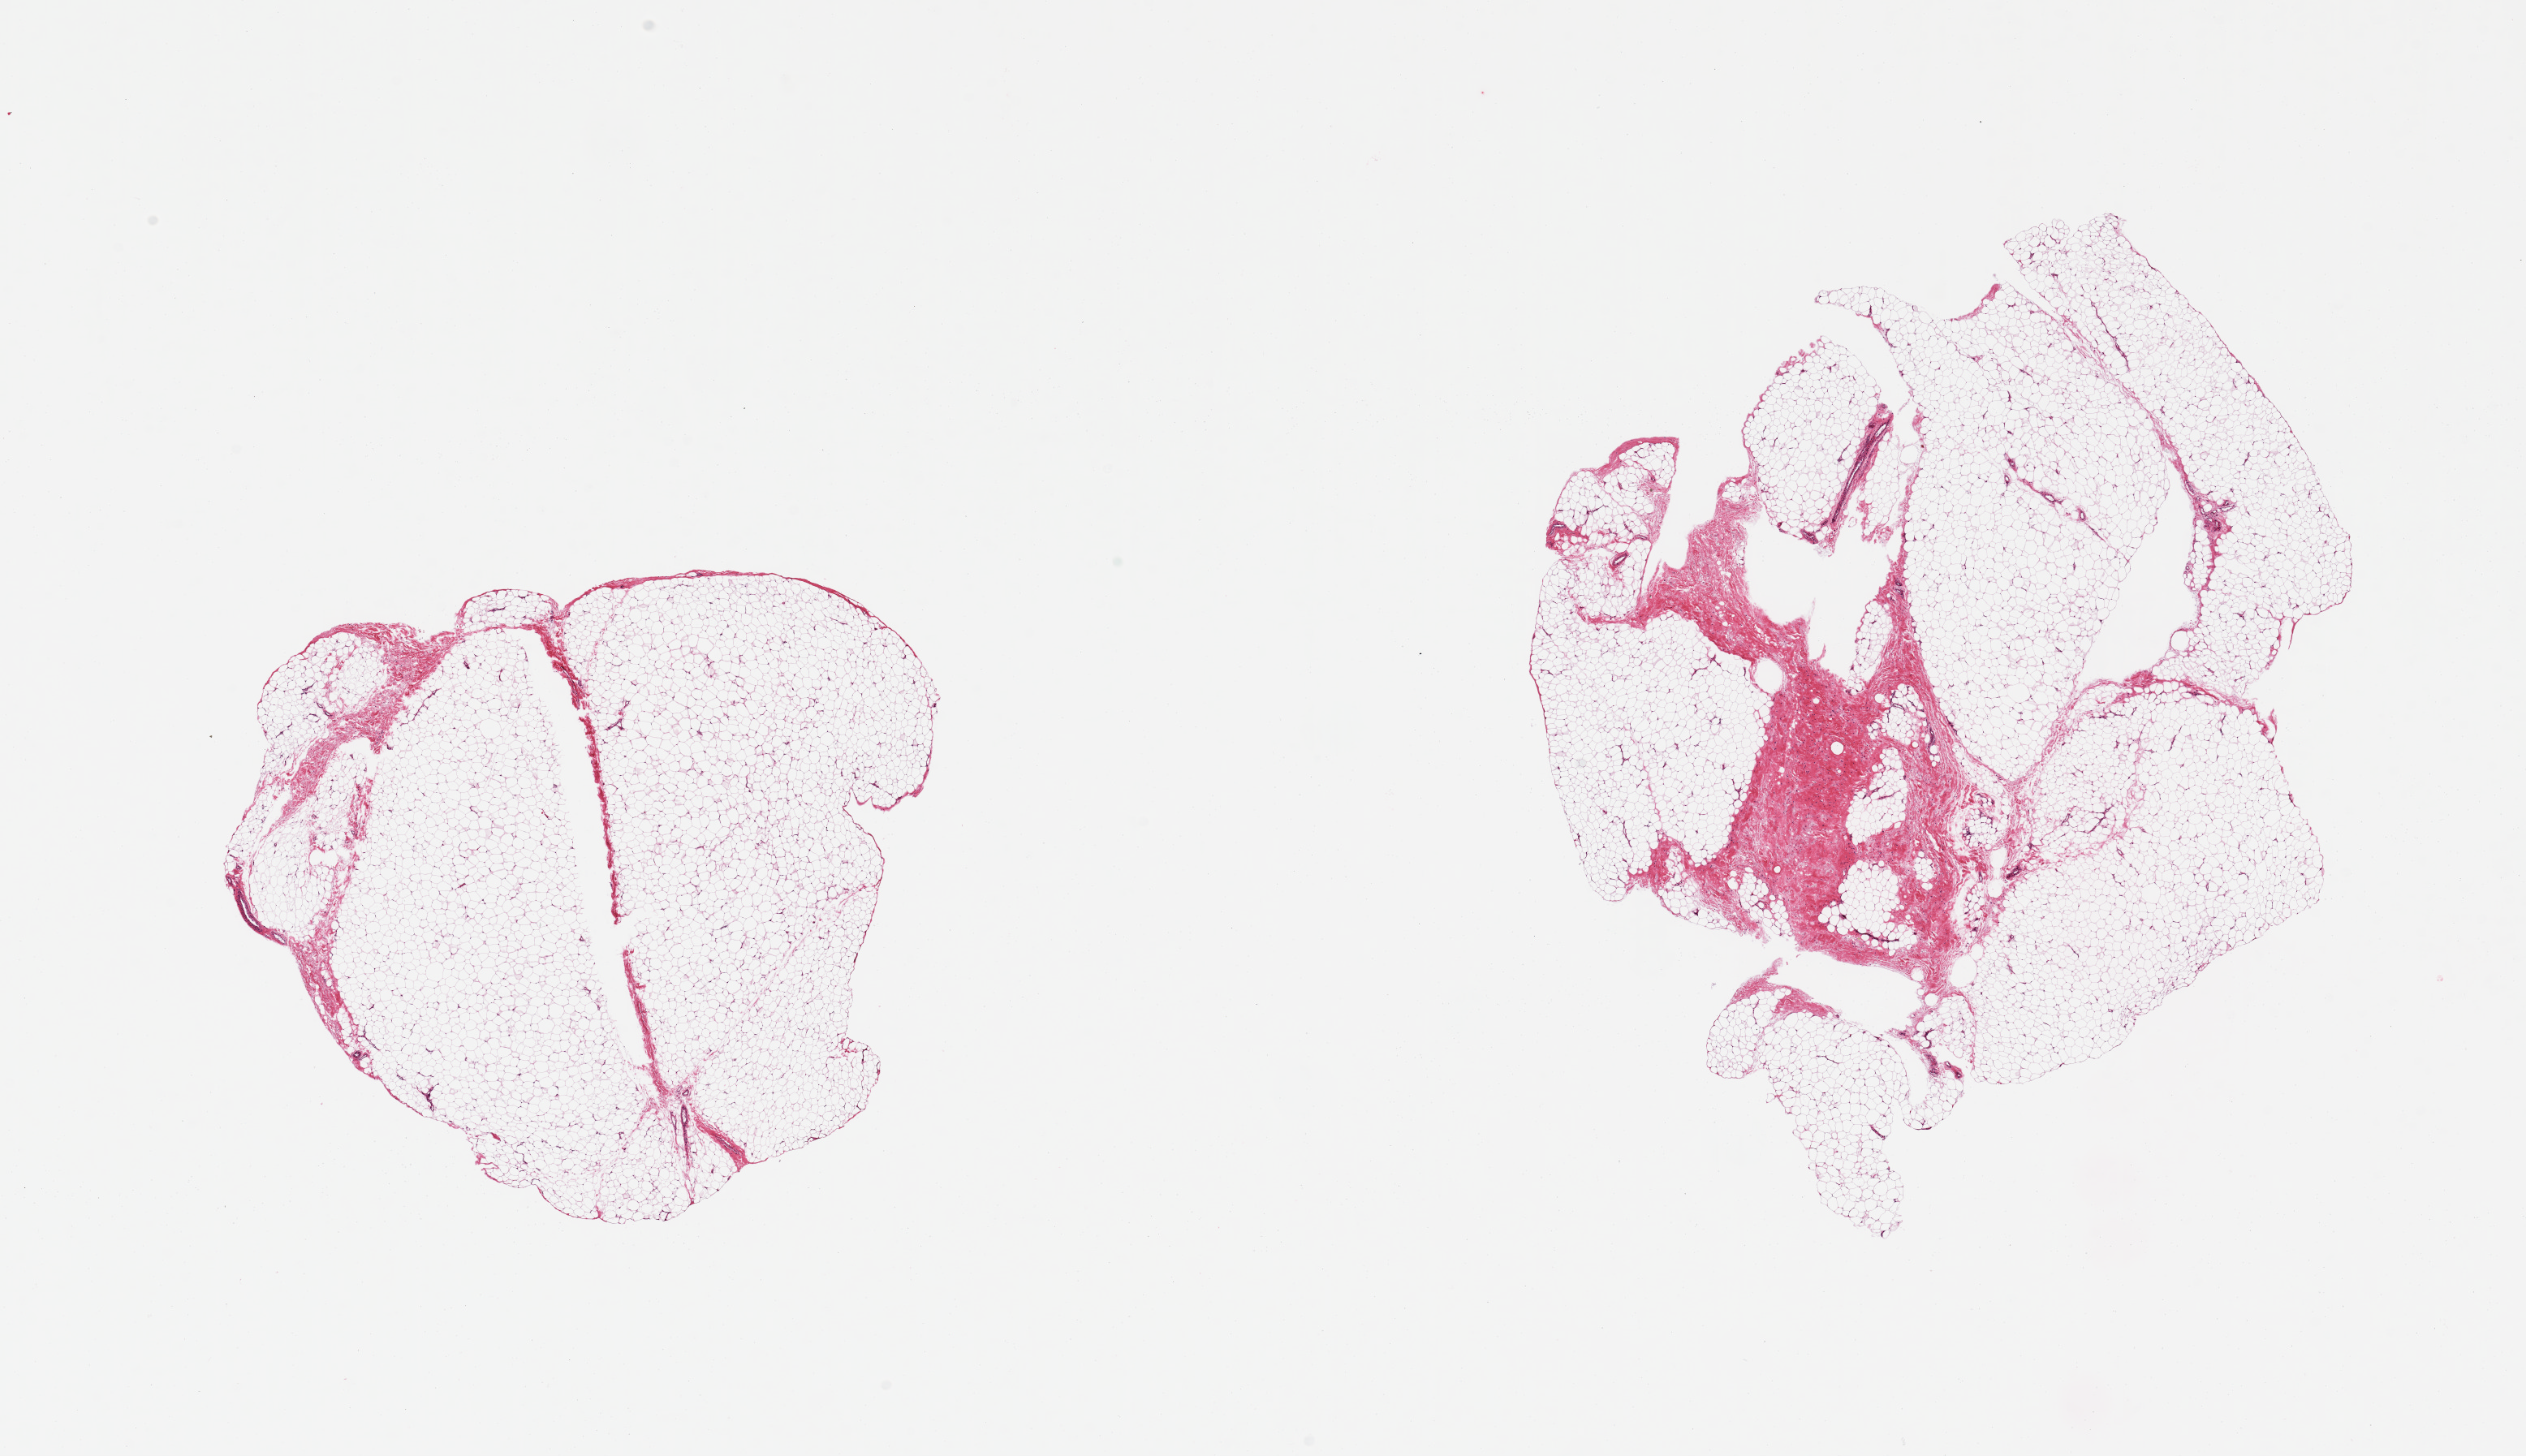
Digitized haematoxylin and eosin-stained section, brightfield — a low-resolution overview of the entire scanned area, about 24.6 x 14.2 mm. PAXgene-fixed paraffin-embedded (PFPE) section. Sampled site (target tissue): adipose tissue. Donor tissue sample. Male donor.
* review note (as recorded): 2 pieces; 1 with 5% other with 20% fibrous content